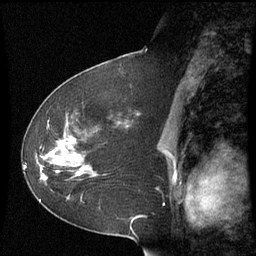
Breast MRI (dynamic contrast-enhanced), one sagittal slice. Position 33 of 60 along the scan axis. Dynamic contrast-enhanced series, image 2 of 3 at this slice position (ordered by acquisition). 1.5 T. TE 4.2 ms, TR 8.9 ms. 256 × 256 image matrix, field of view 210 × 210 mm. Female patient, age 51 years. From the clinical record (not read from this slice): setting: breast cancer imaged before/during neoadjuvant chemotherapy; receptor status: HR-positive, HER2-negative.
Structures marked on this image (semi-automatic segmentation, software-assisted and operator-edited):
- analysis volume of interest (the breast-tissue region the enhancement analysis was run in; not a lesion): bounding box [x1, y1, x2, y2] px = [50, 120, 99, 181]
- tumour enhancement mask (voxels above the 70 % enhancement threshold inside the analysis volume of interest): [77, 173, 79, 175]